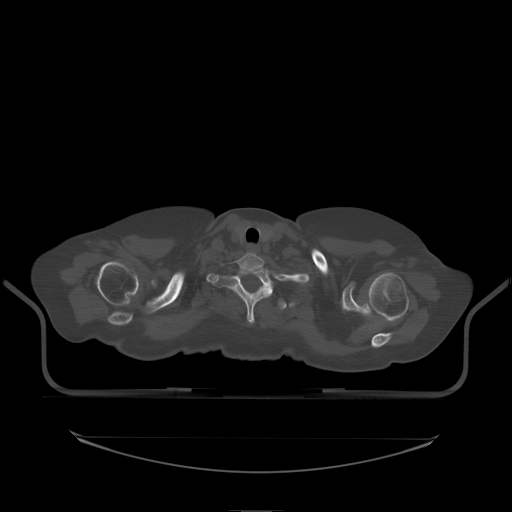
CT including the spine, one axial slice. Slice 187 of 242 in the series (ordered by position). Bone window (W 1800 / L 400 HU). 2.5 mm slice thickness. 512 × 512 image matrix, field of view 500 × 500 mm. Female patient, age 53 years. Case-level facts recorded for this patient, not image findings: primary cancer: lung; vertebrae with lytic lesions (as recorded): T7, L1.
Annotated regions visible in this slice (semi-automatic segmentation, software-assisted and operator-edited):
- T1 vertebra: bounding box [x1, y1, x2, y2] px = [214, 270, 273, 324]
- T2 vertebra: [234, 291, 287, 310]